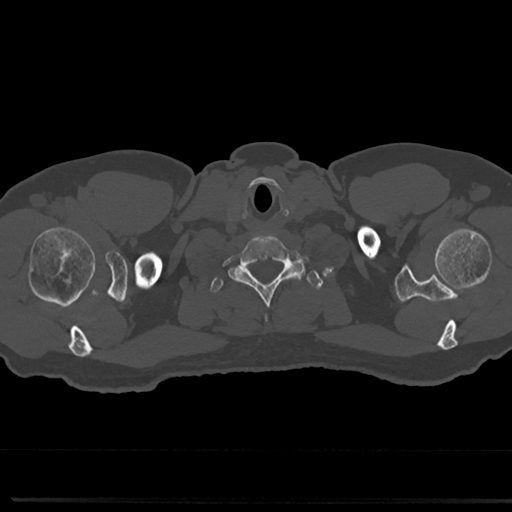
CT including the spine, one axial slice; position 698 of 817 along the scan axis; 120 kVp; bone window (W 1800 / L 400 HU); 0.5 mm slice thickness; 512 × 512 image matrix, field of view 355 × 355 mm. Patient: male, 61 years. From the clinical record (not read from this slice): primary cancer: prostate.
Structures marked on this image (semi-automatically segmented with operator editing):
- T1 vertebra: bounding box (x1, y1, x2, y2) in pixels: (209, 268, 319, 296)